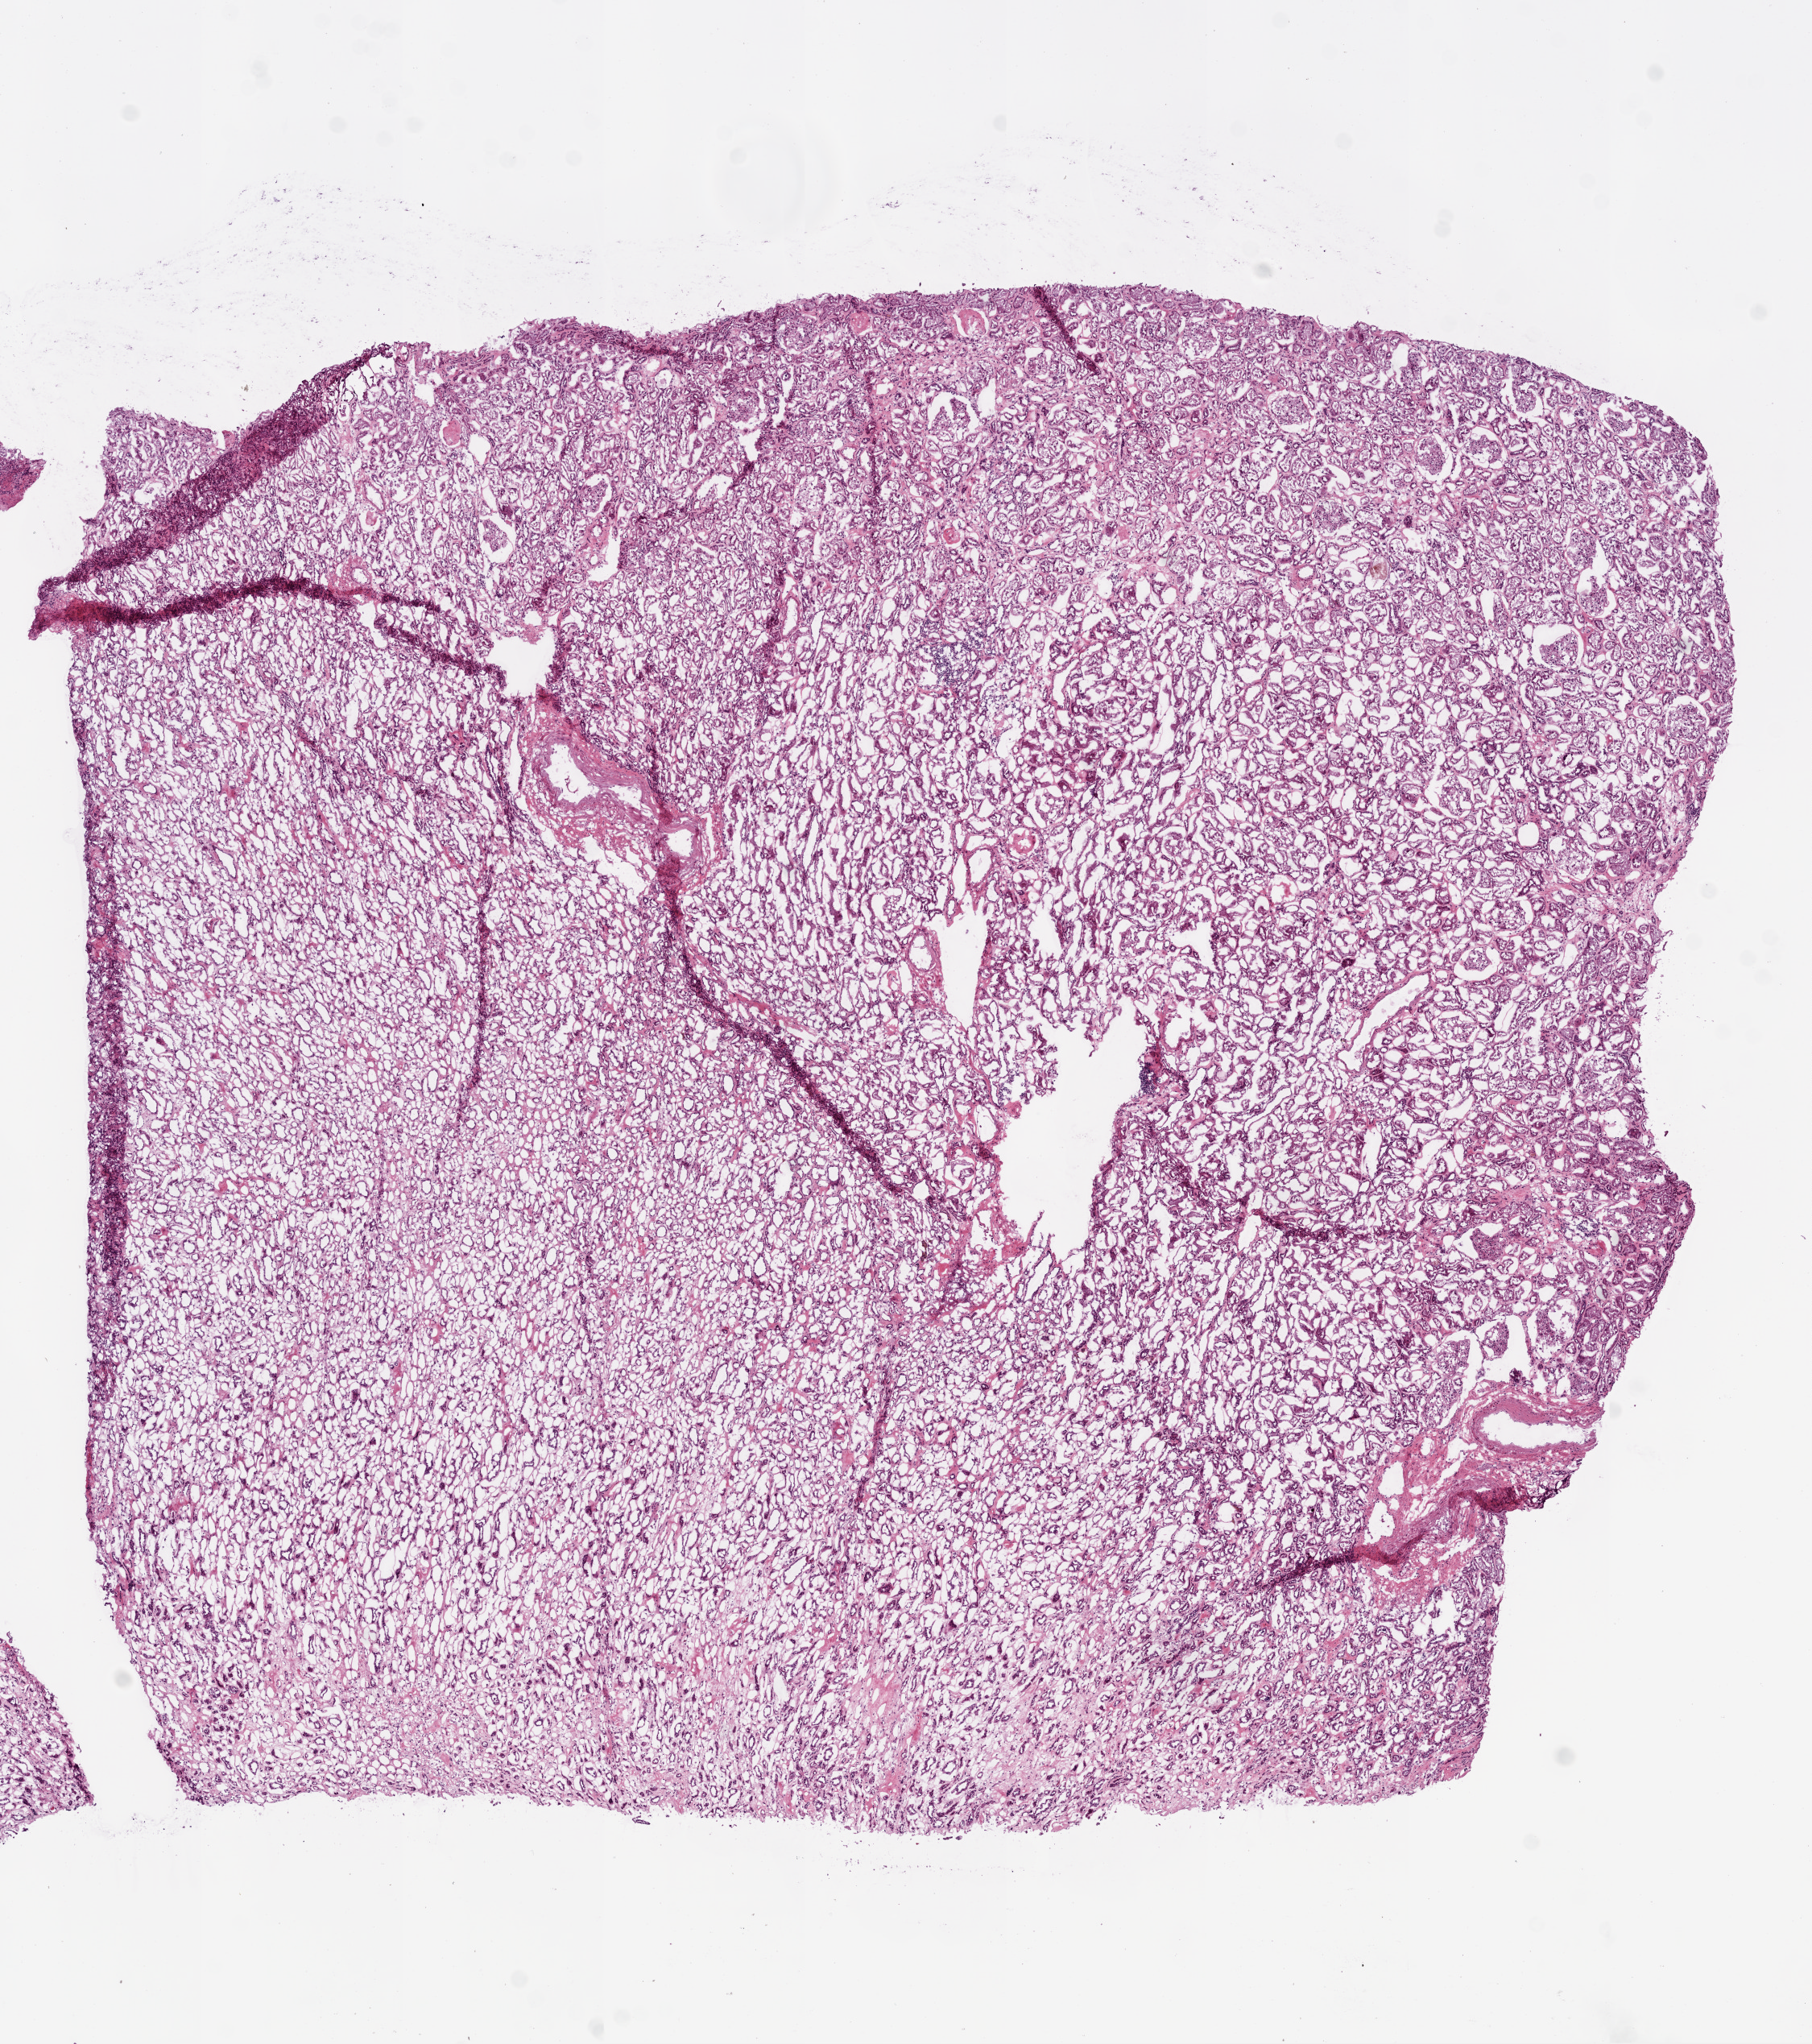
Whole-slide histology image, Hematoxylin and eosin (H&E) stained, a low-resolution overview of the entire scanned area, about 9.0 x 10.2 mm (acquisition: 20x scan); frozen section; kidney, solid tissue normal (non-tumour tissue) sample. Male, age 60 years at initial diagnosis.
* this section: solid tissue normal (non-tumour) sample from the same patient
* patient diagnosis: Clear cell adenocarcinoma, NOS